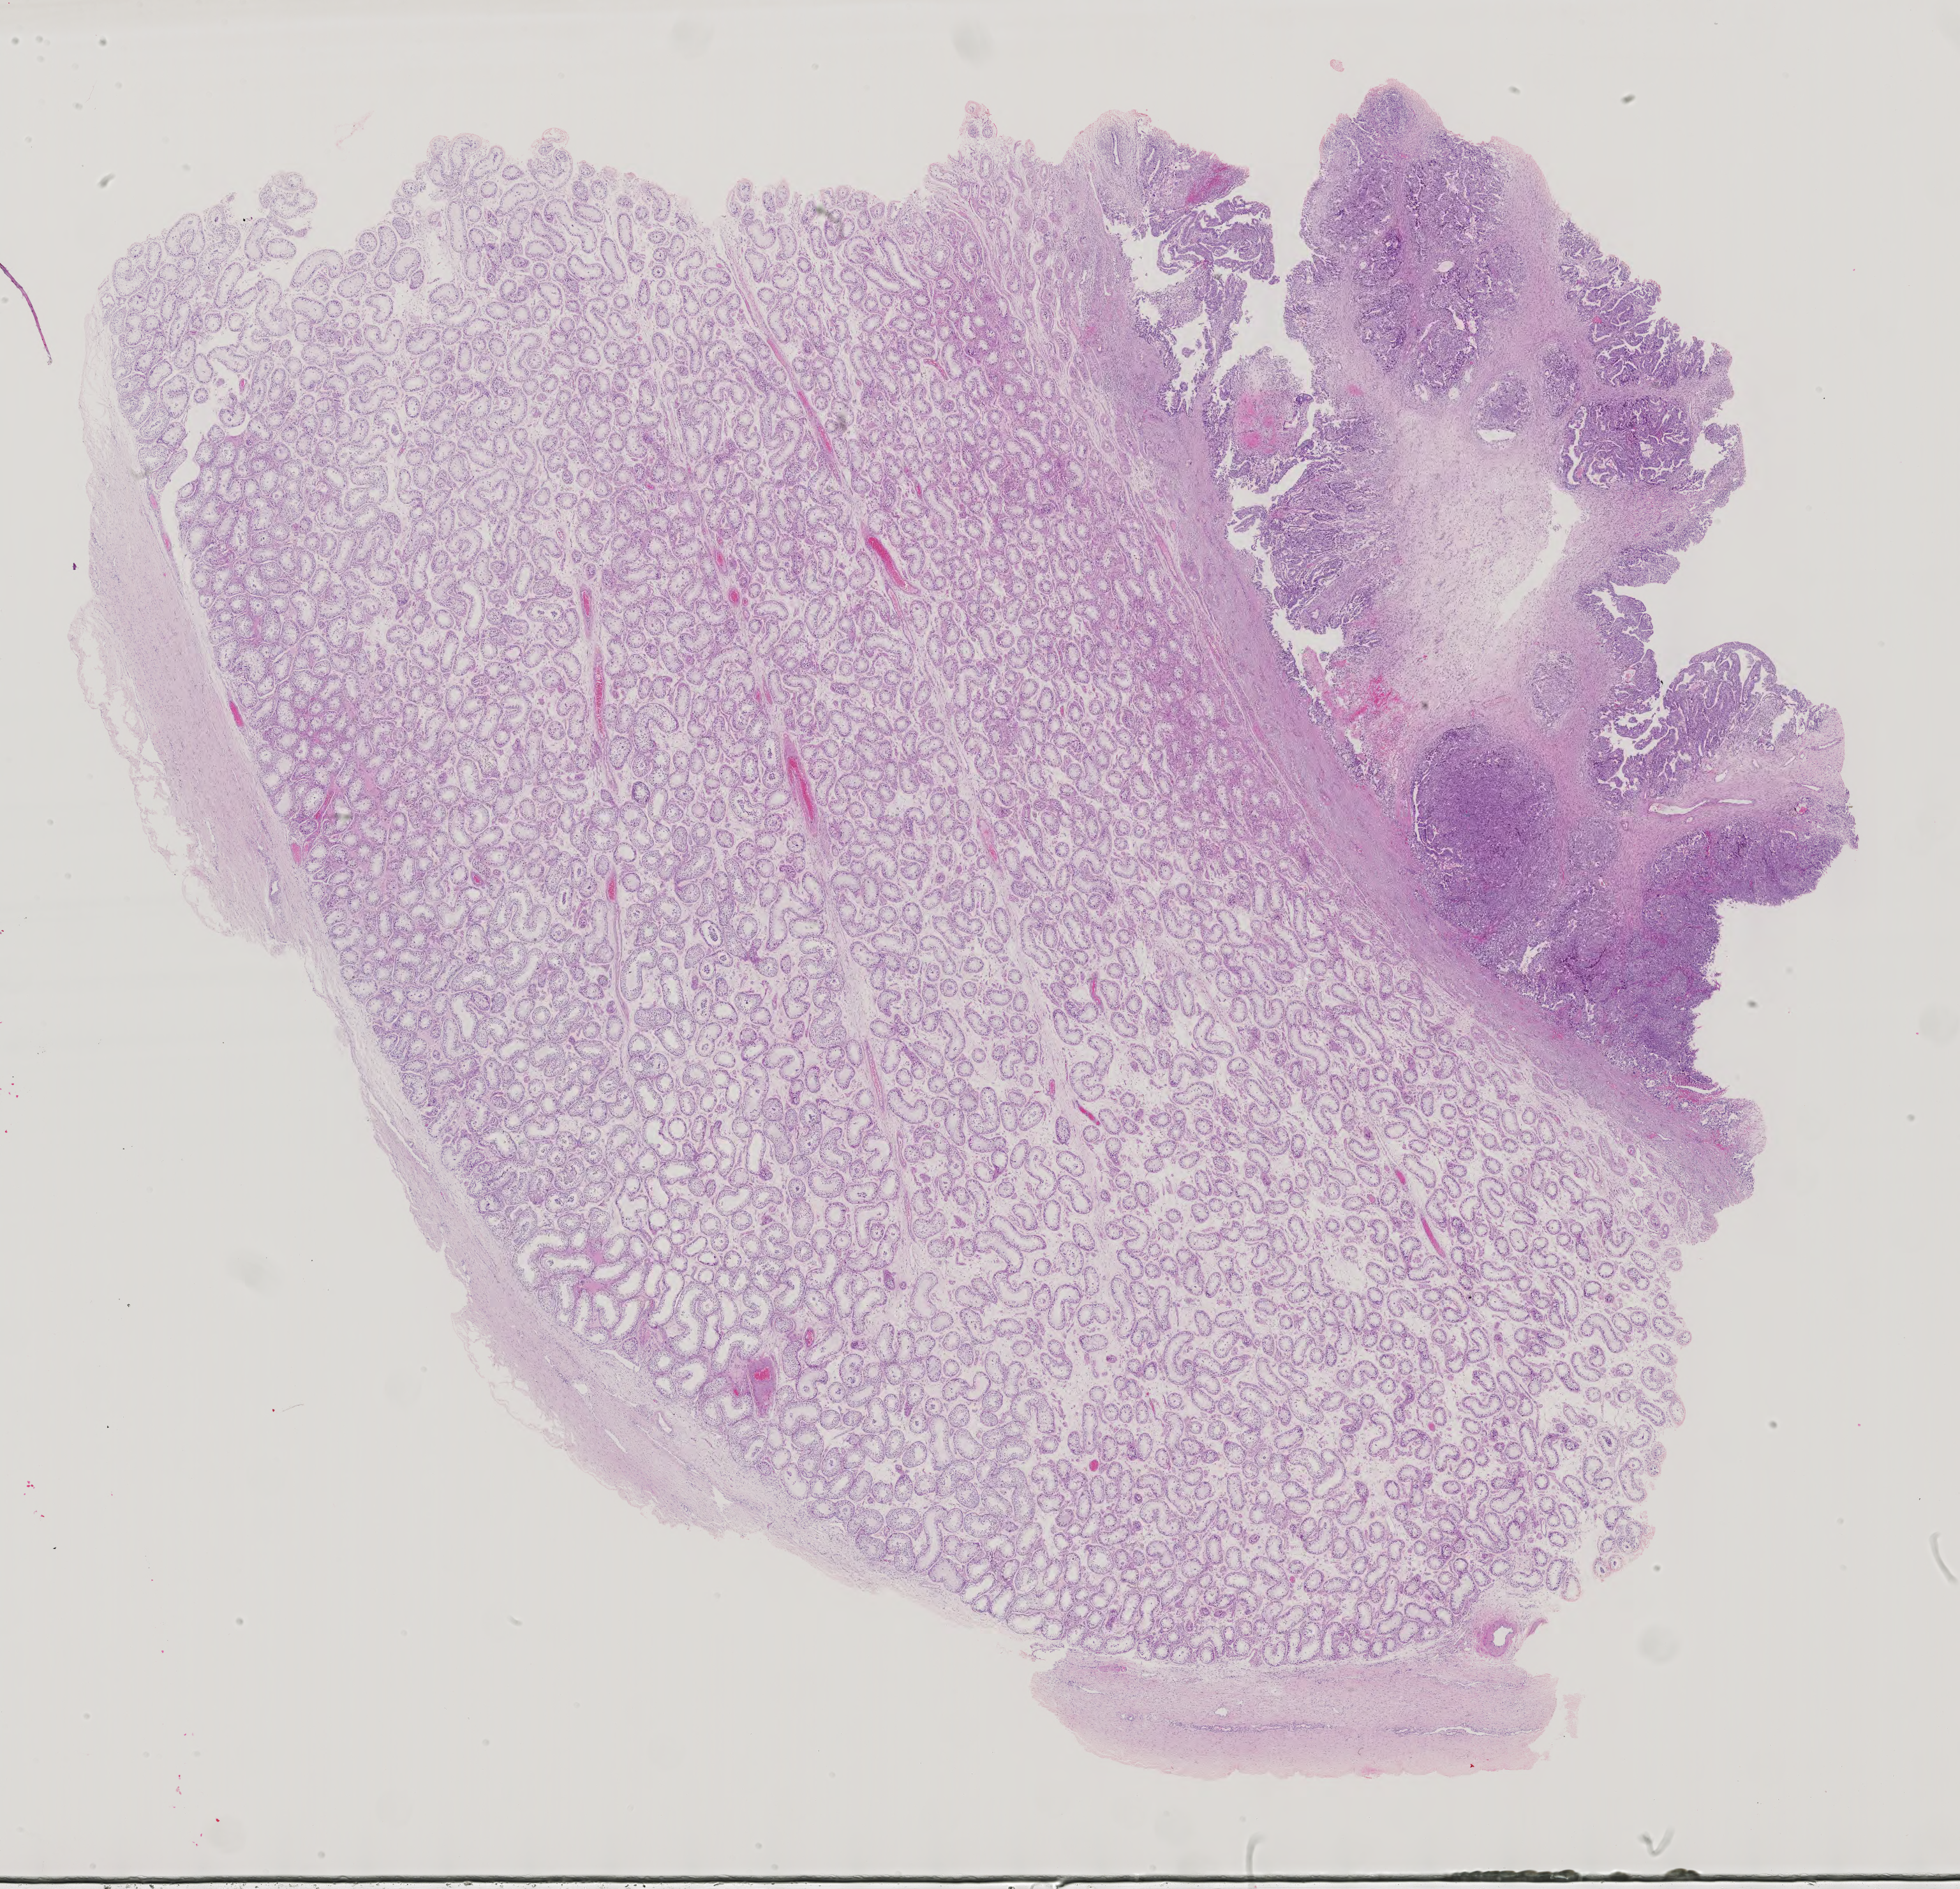
Whole-slide histology image, Hematoxylin and eosin (H&E) stained — low-resolution overview of the scanned area, about 22.4 x 21.6 mm. Patient sex: male.
Specimen: FFPE section; primary tumour sample from the testis.